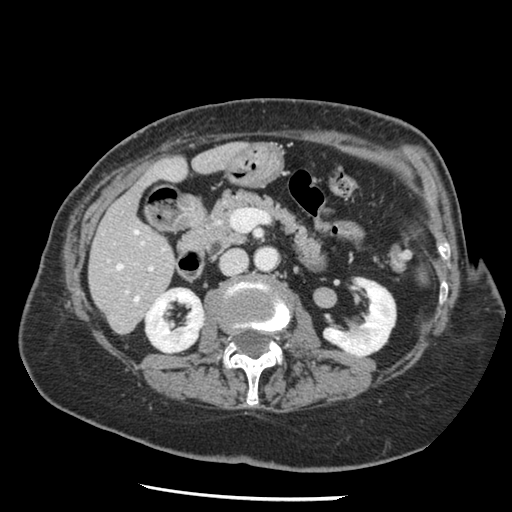
Contrast-enhanced abdominal CT, one axial slice; position 55 of 148 along the scan axis; reconstruction kernel STANDARD; 120 kVp; intravenous contrast given; soft-tissue window (W 400 / L 40 HU); 2.5 mm slice thickness; 512 × 512 image matrix, field of view 330 × 330 mm. Female patient, age 85 years. From the clinical record (not read from this slice): diagnosis: colorectal cancer liver metastases, imaged before liver resection; multiple liver metastases: no; largest metastasis: 0.9 cm; disease in both lobes: no.
Outlined on this slice (outlined manually by an expert reader):
- hepatic veins: bounding box <116,230,138,301> (left, top, right, bottom; pixels)
- liver: <90,144,241,333>
- planned liver remnant (the part of the liver to remain after resection): <90,144,241,330>